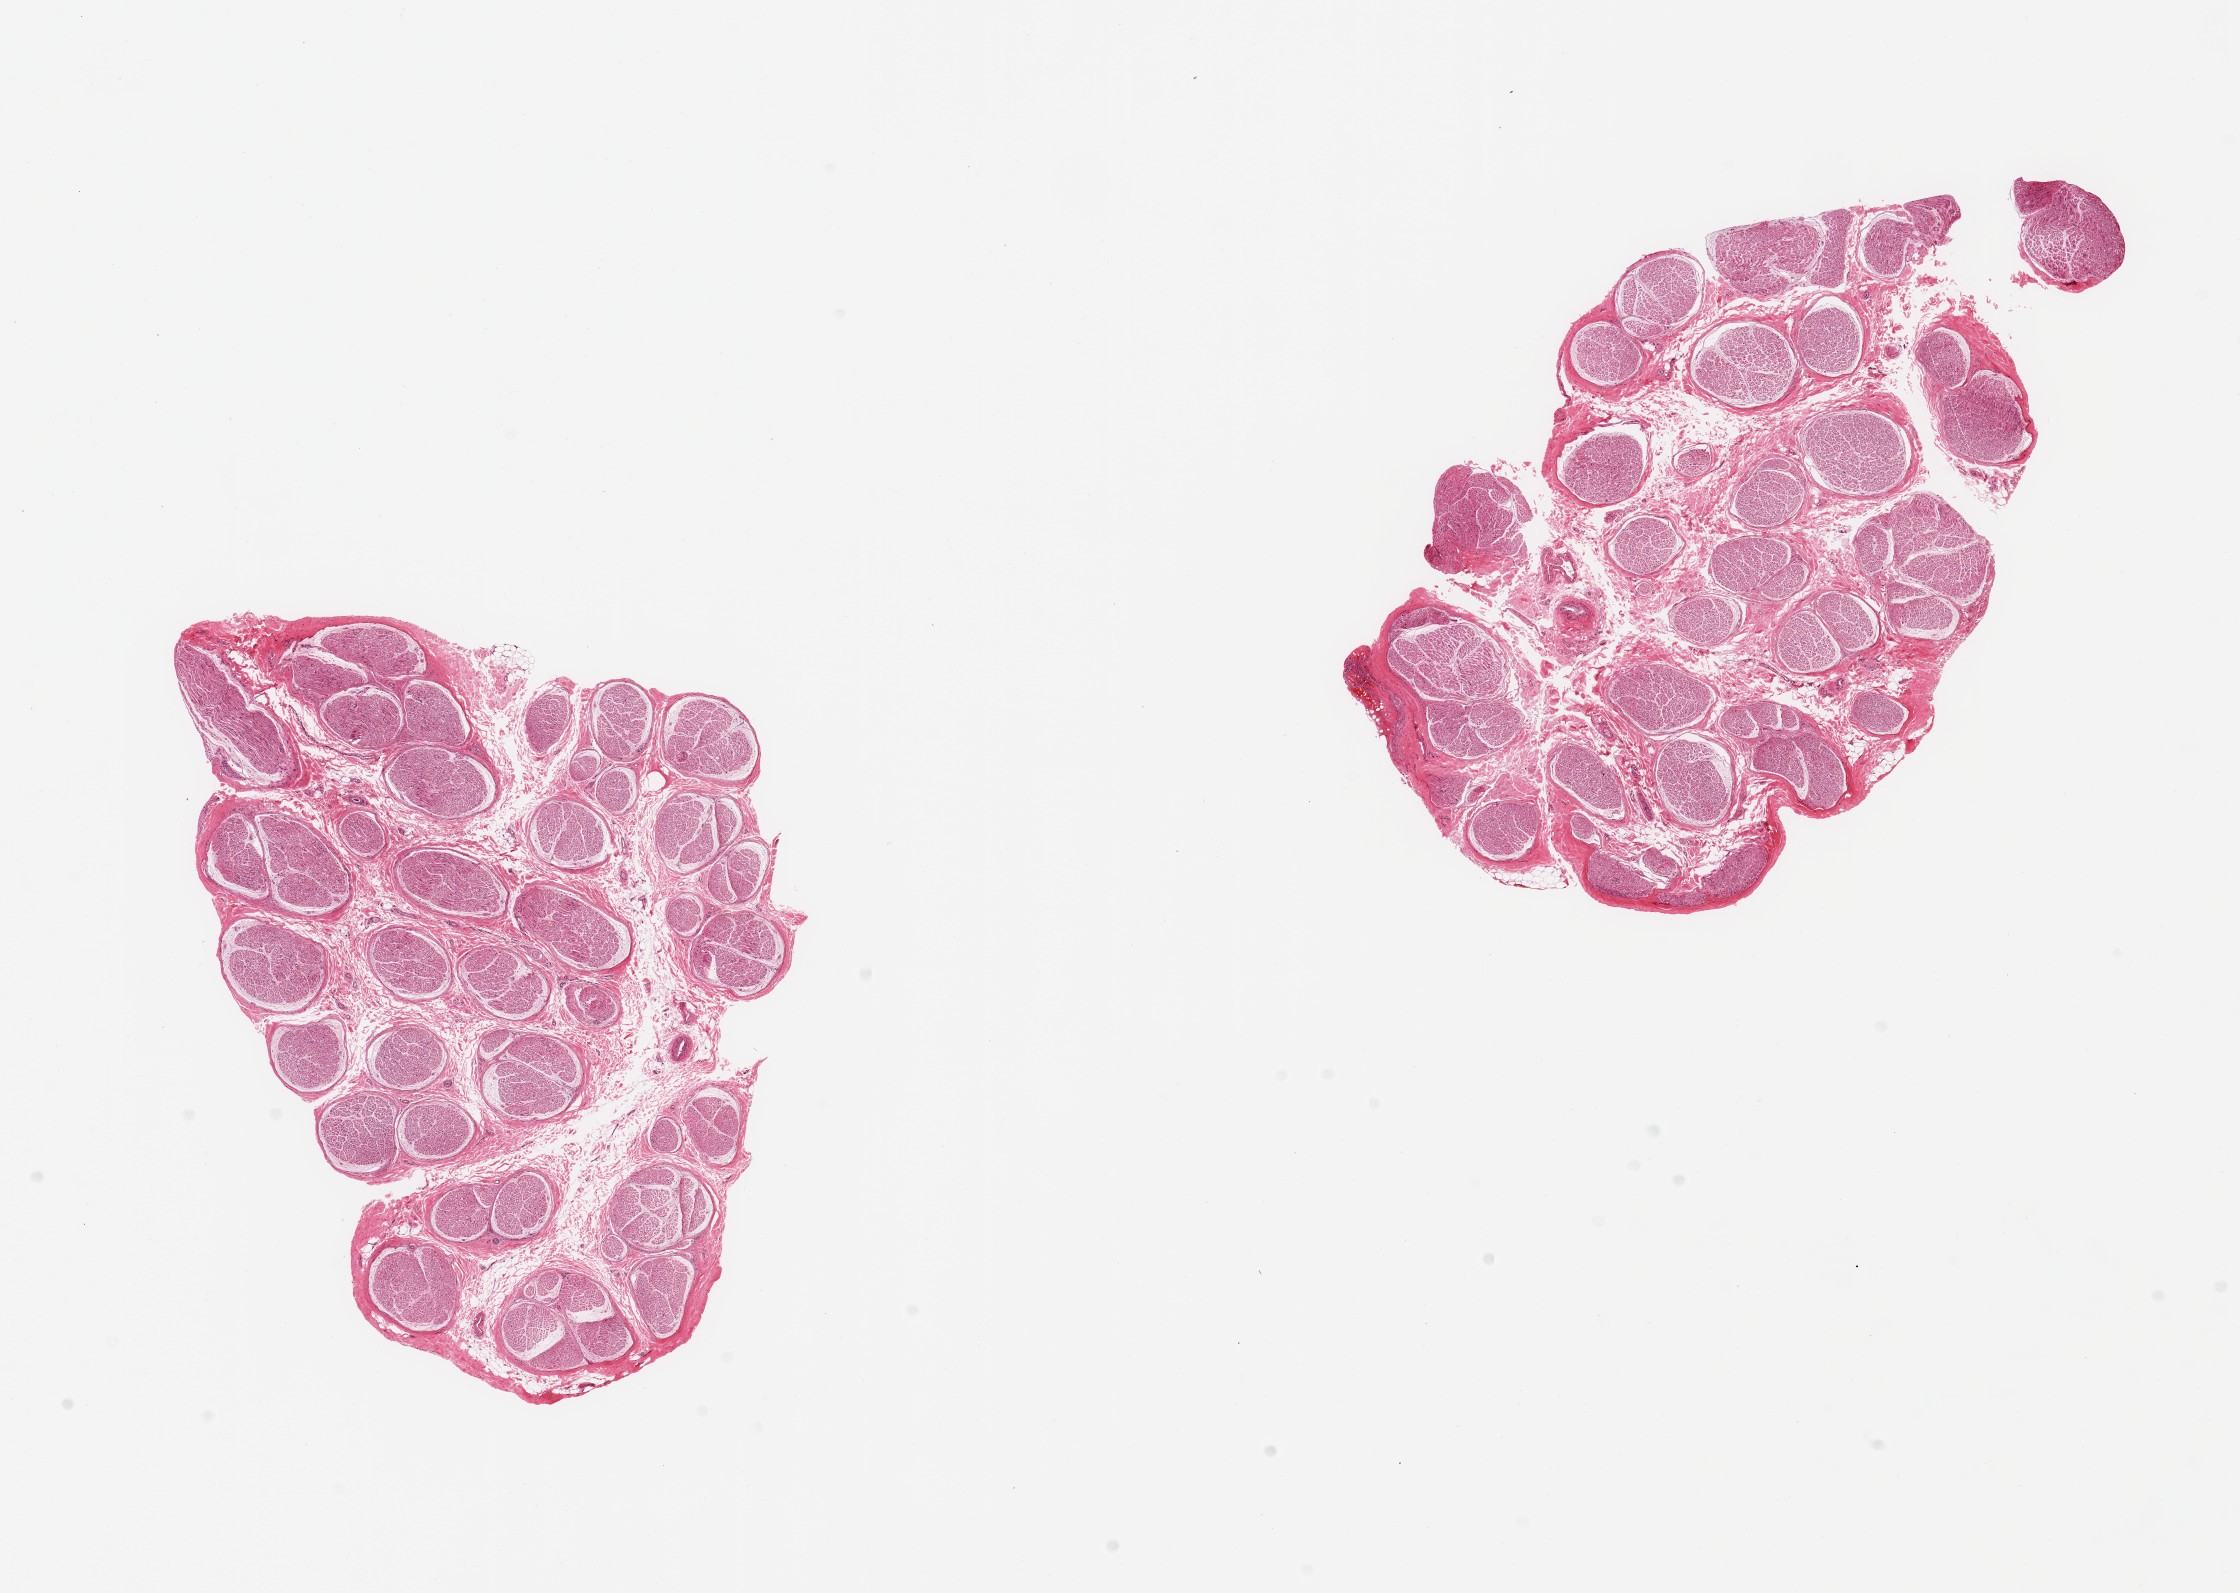
Whole-slide image, hematoxylin and eosin (H&E) stain, a low-resolution overview of the entire scanned area, about 17.7 x 12.6 mm. PAXgene-fixed paraffin-embedded (PFPE) section. Sampled site (target tissue): tibial nerve. Tissue donor sample. Donor: female.
Reviewer comment on this tissue sample: 2 pieces; well trimmed, minimal internal fat.